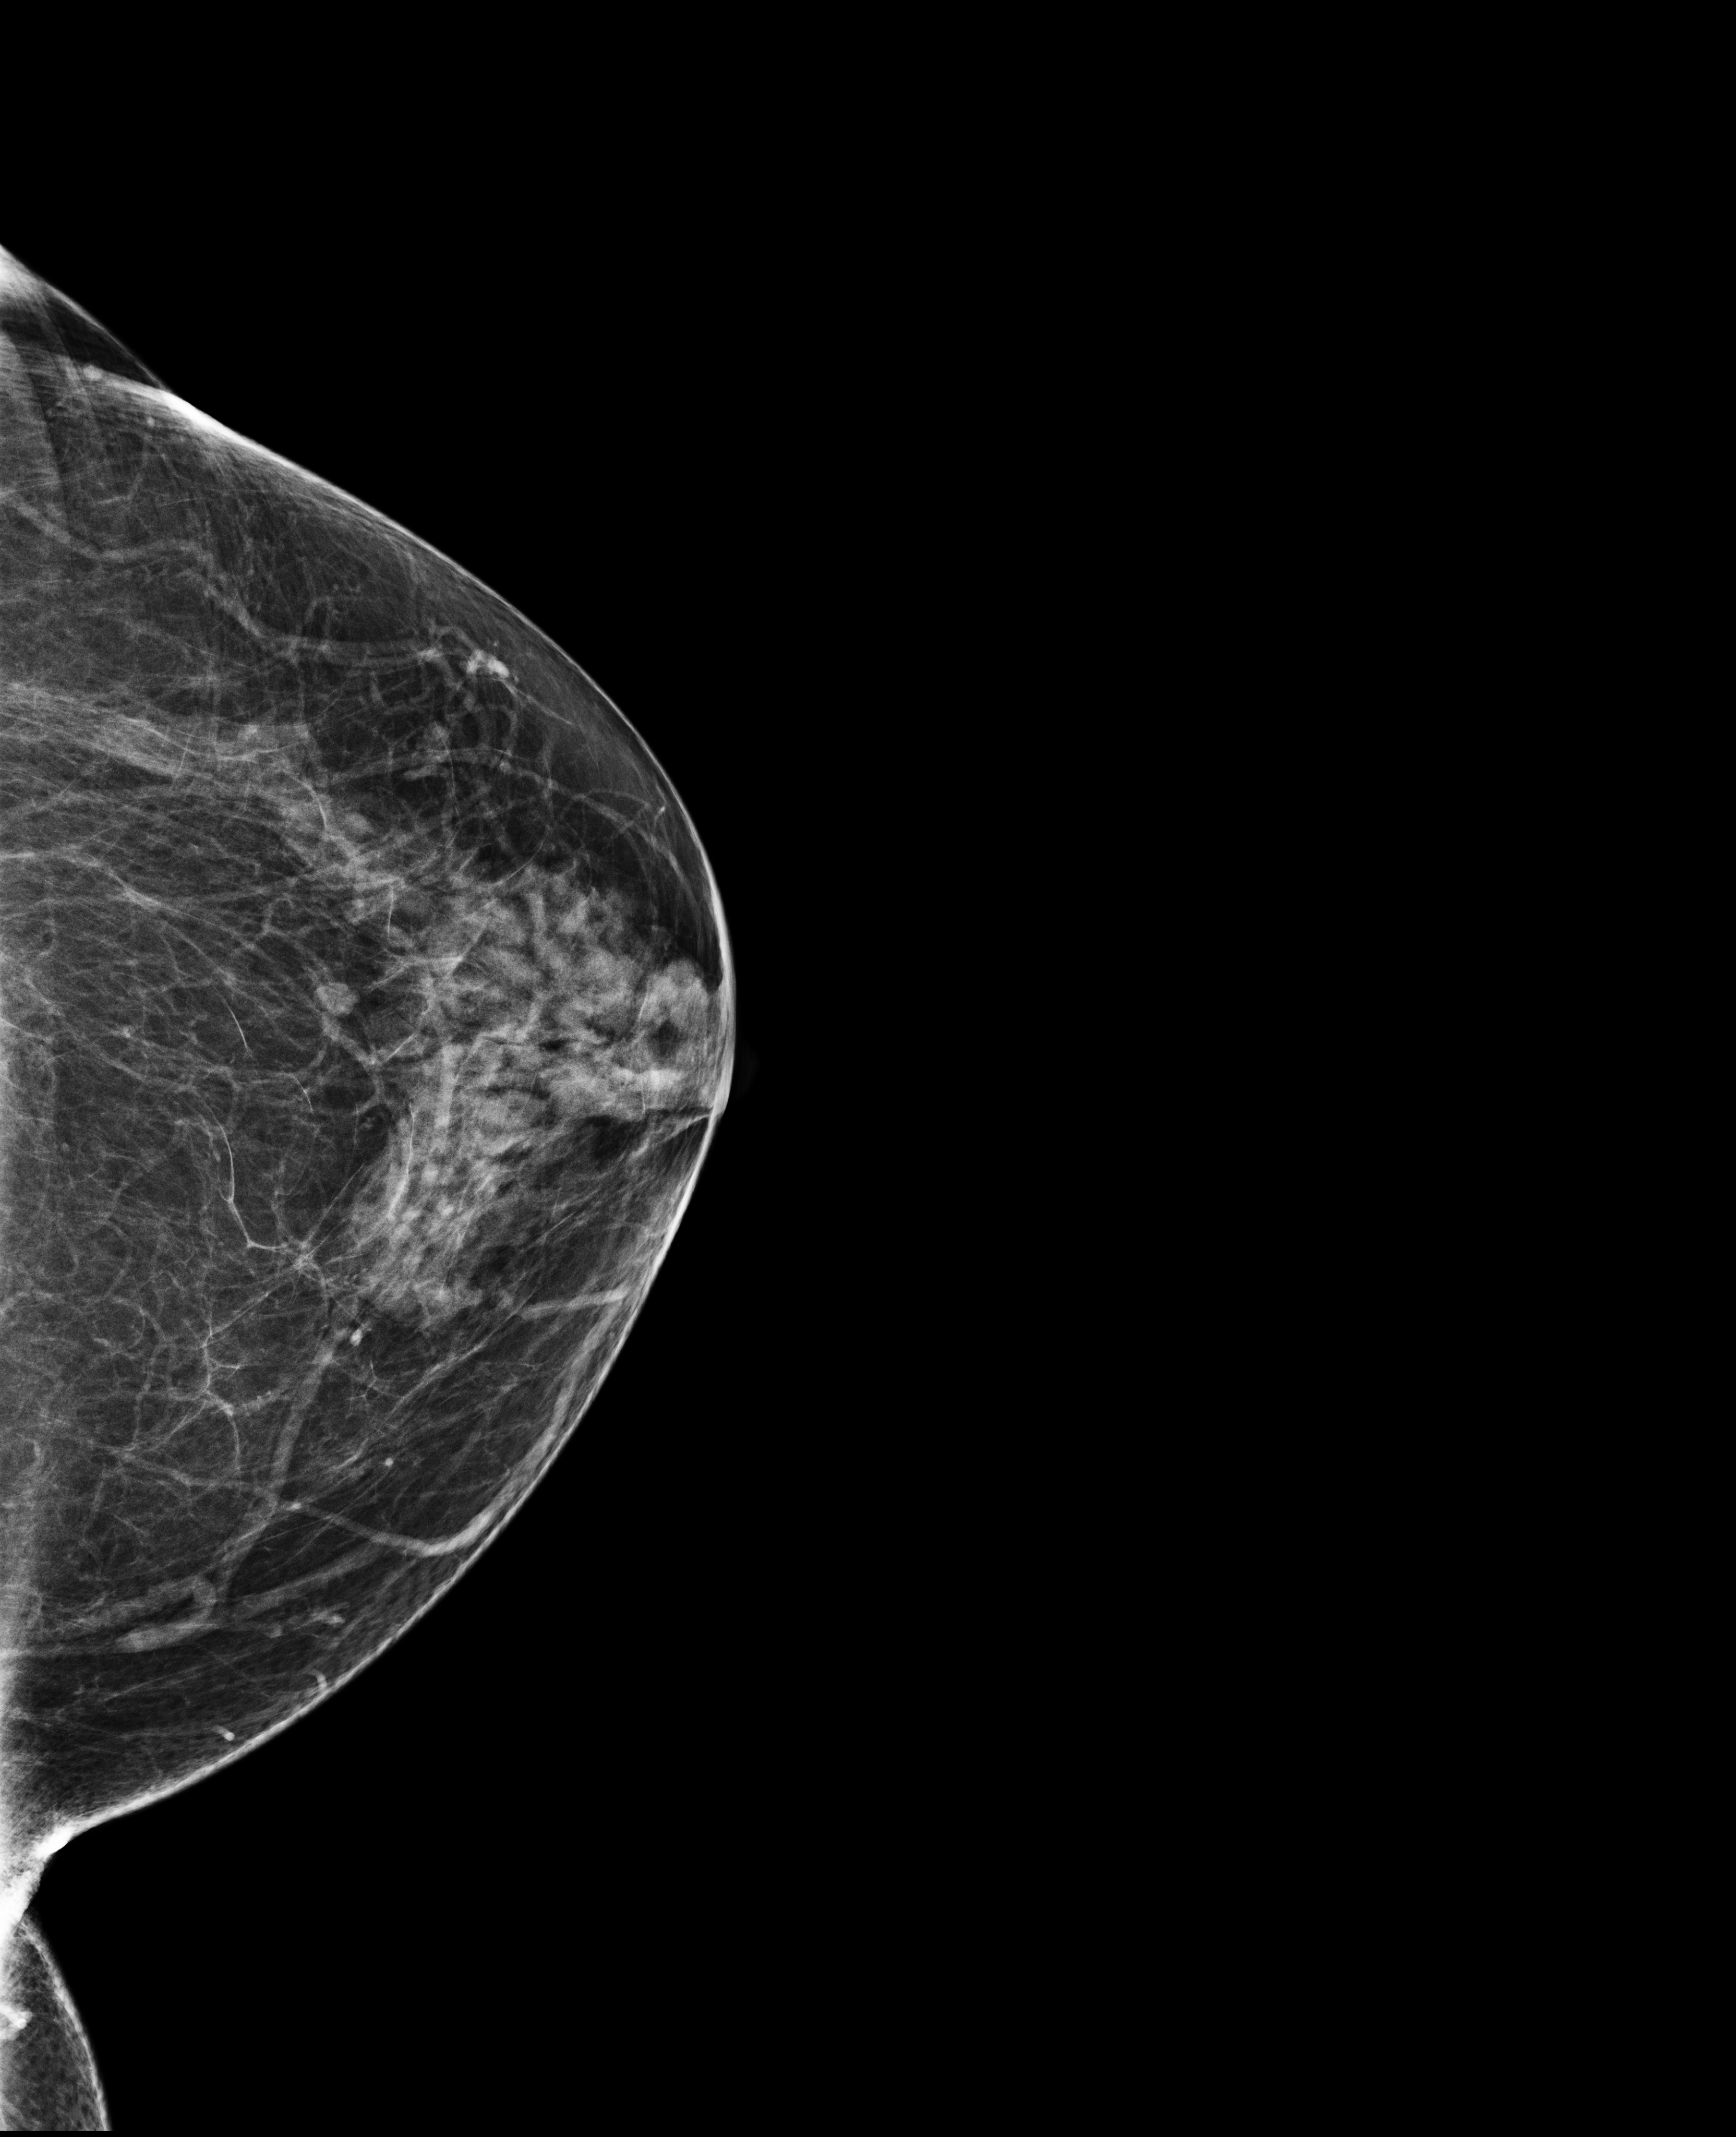
Annual screening mammography examination.
Image type: full-field digital mammogram. Breast: left. Projection: cranio-caudal projection.